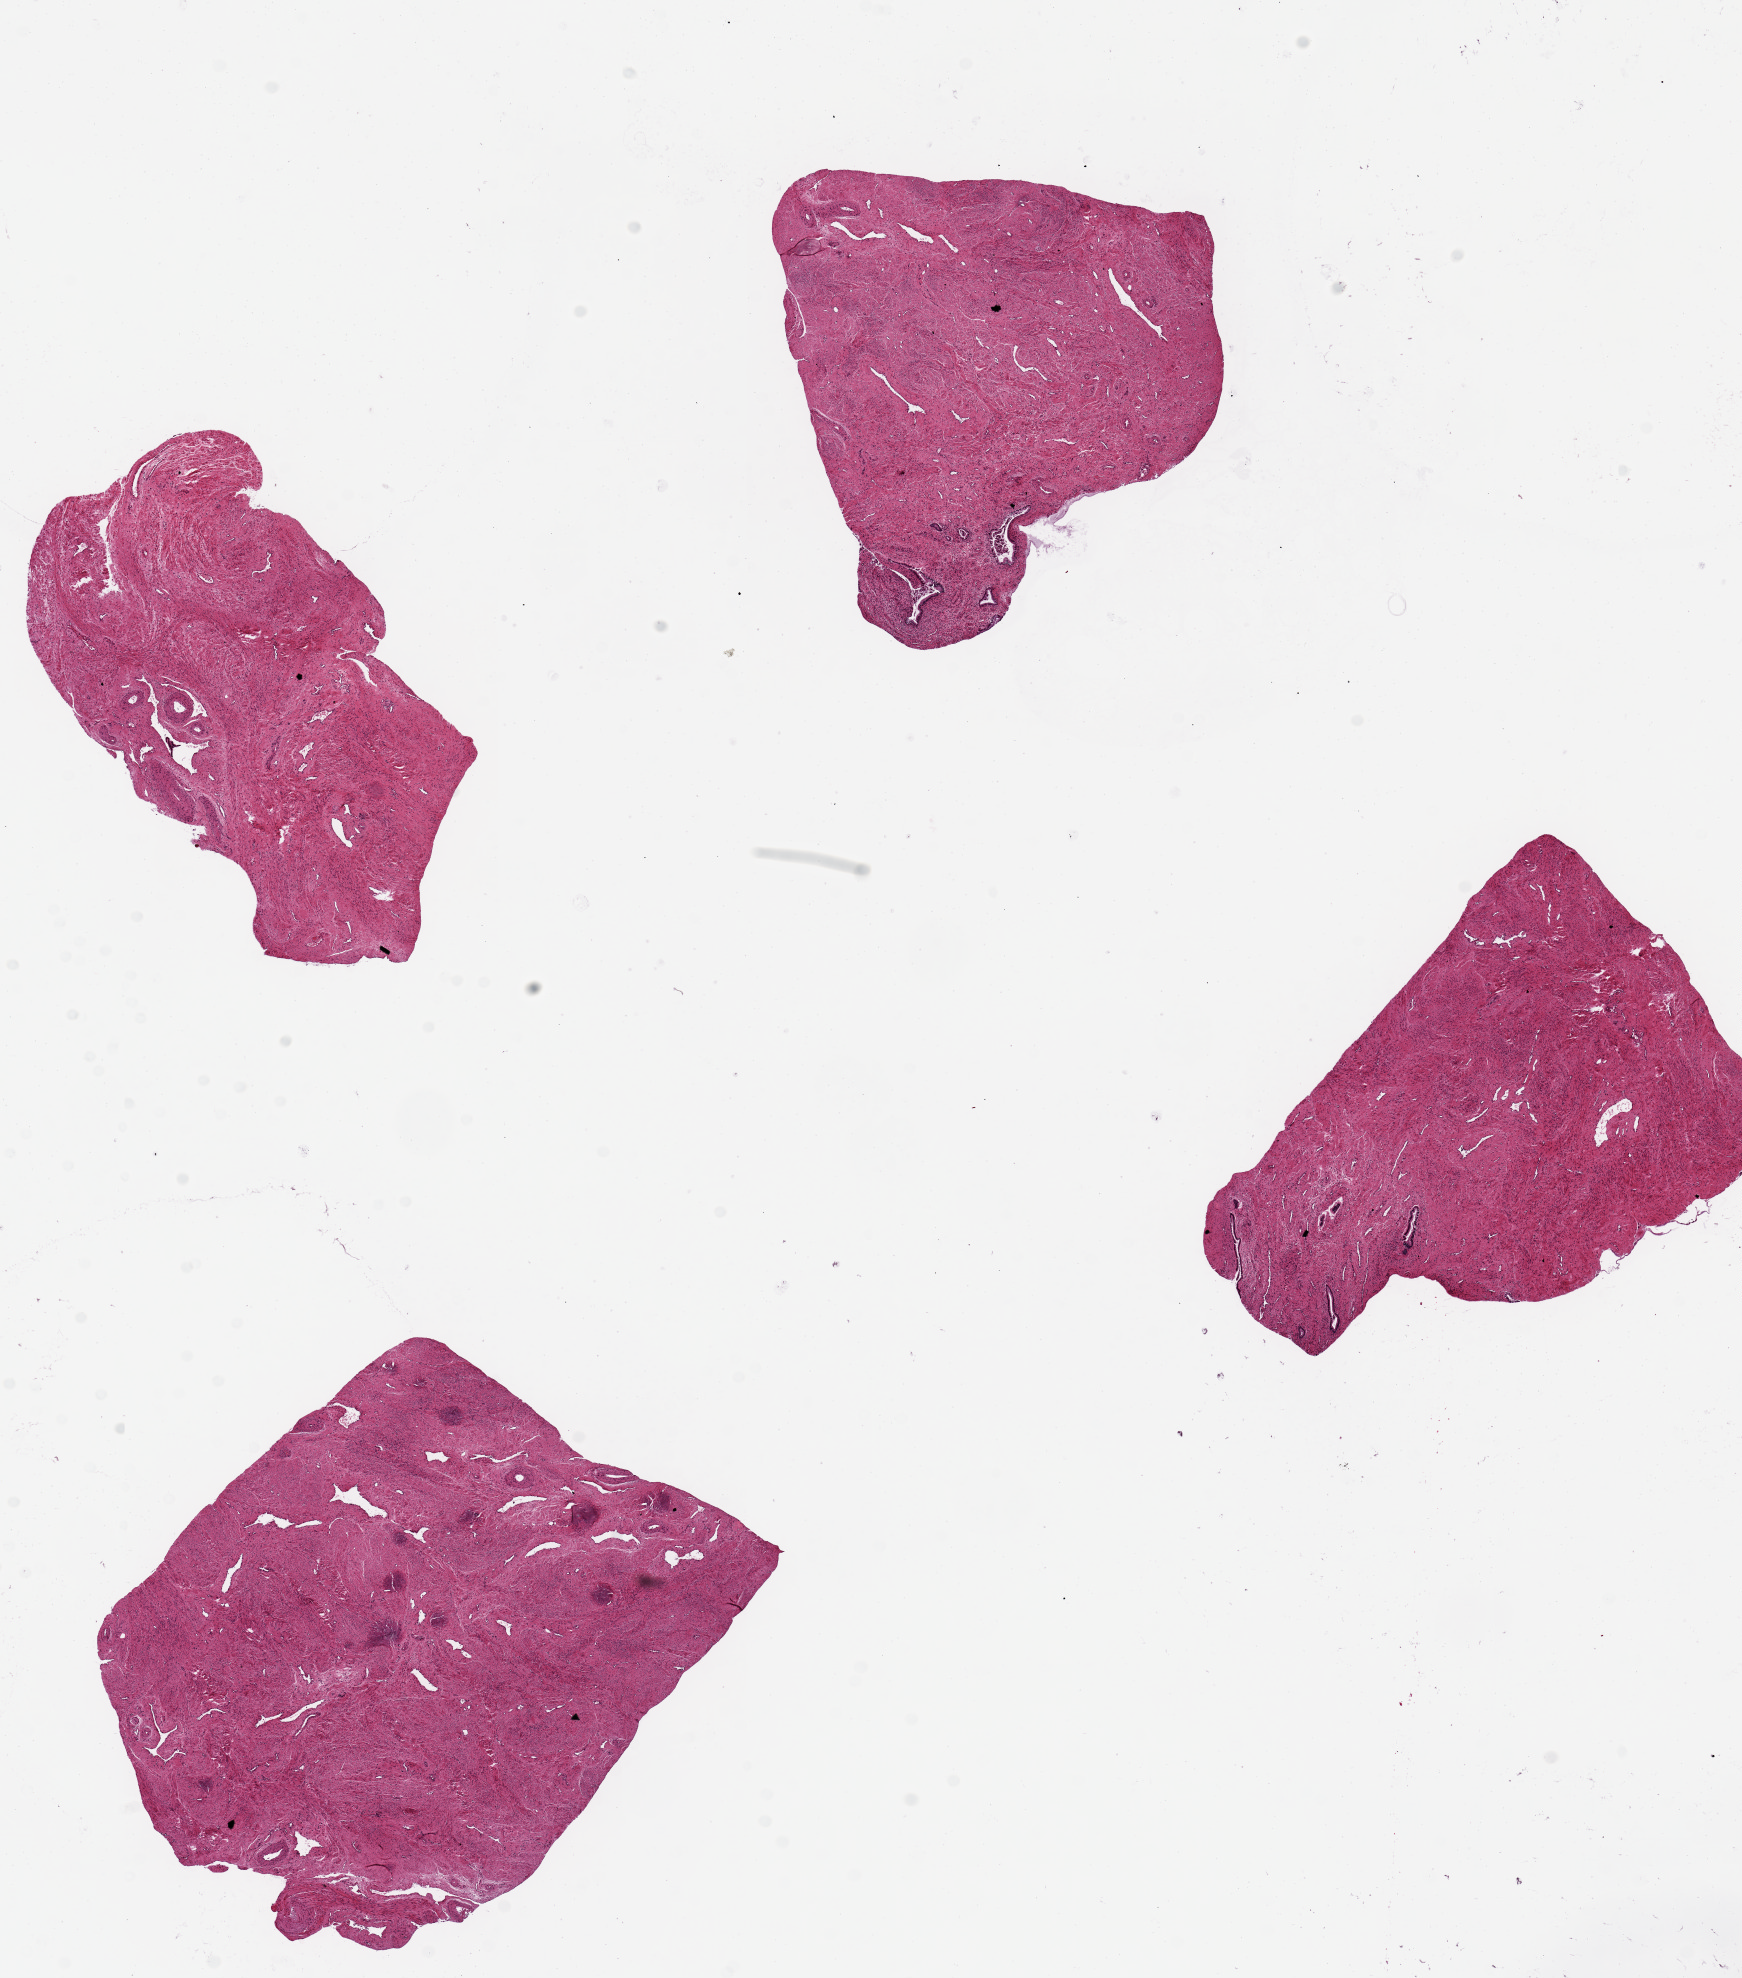
Digitized H&E-stained section, brightfield — shown as a low-resolution overview of the whole scanned area (about 13.8 x 15.6 mm), PAXgene-fixed paraffin-embedded (PFPE) section, target tissue: endocervix, donor tissue sample. Donor sex: female.
Review note (as recorded): 4 pieces ~4x3mm; Few minute endocervical glands noted.